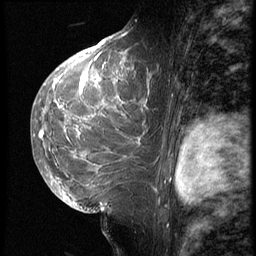
Breast MRI (dynamic contrast-enhanced), one sagittal slice; position 36 of 62 along the scan axis; 3 images stored at this slice position (order not interpretable as contrast timing); 1.5 T; TE 4.2 ms, TR 9 ms; 2.5 mm slice thickness; 256 × 256 image matrix, field of view 180 × 180 mm. Patient: female, 28 years. From the clinical record (not read from this slice): setting: breast cancer imaged before/during neoadjuvant chemotherapy.
Structures marked on this image (semi-automatic segmentation, software-assisted and operator-edited):
- analysis volume of interest (the breast-tissue region the enhancement analysis was run in; not a lesion): box from (x=42, y=45) to (x=161, y=207) px
- tumour enhancement mask (voxels above the 140 % enhancement threshold inside the analysis volume of interest): (x=42, y=46)–(x=156, y=189)